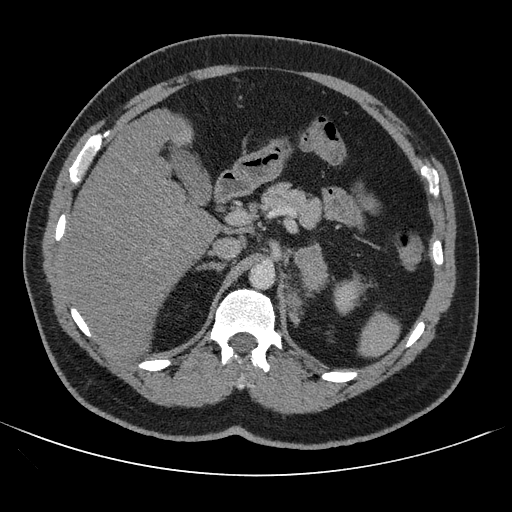
Contrast-enhanced abdominal CT, one axial slice; slice 67 of 121 in the series (ordered by position); intravenous contrast given; soft-tissue window (W 400 / L 40 HU); 512 × 512 image matrix. Patient: male, 53 years. From the clinical record (not read from this slice): diagnosis: adrenocortical carcinoma; tumour side: left adrenal; tumour size at pathology: 7.9 cm; Ki-67 index: 20 %; stage (as recorded): 2.
Annotated regions visible in this slice (semi-automatically segmented with operator editing):
- mass: bounding box <288,245,326,322> (left, top, right, bottom; pixels)